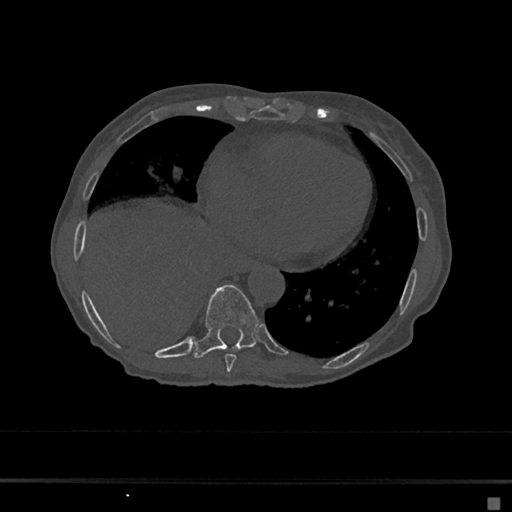
CT including the spine, one axial slice. Position 287 of 797 along the scan axis. Reconstruction kernel Br40s/3. 120 kVp. Bone window (W 1800 / L 400 HU). 0.5 mm slice thickness. 512 × 512 image matrix, field of view 360 × 360 mm. Female patient, age 68 years. Case-level facts recorded for this patient, not image findings: primary cancer: renal.
Outlined on this slice (semi-automatically segmented with operator editing):
- T8 vertebra: bounding box <224,354,236,372> (left, top, right, bottom; pixels)
- T9 vertebra: <193,285,259,358>